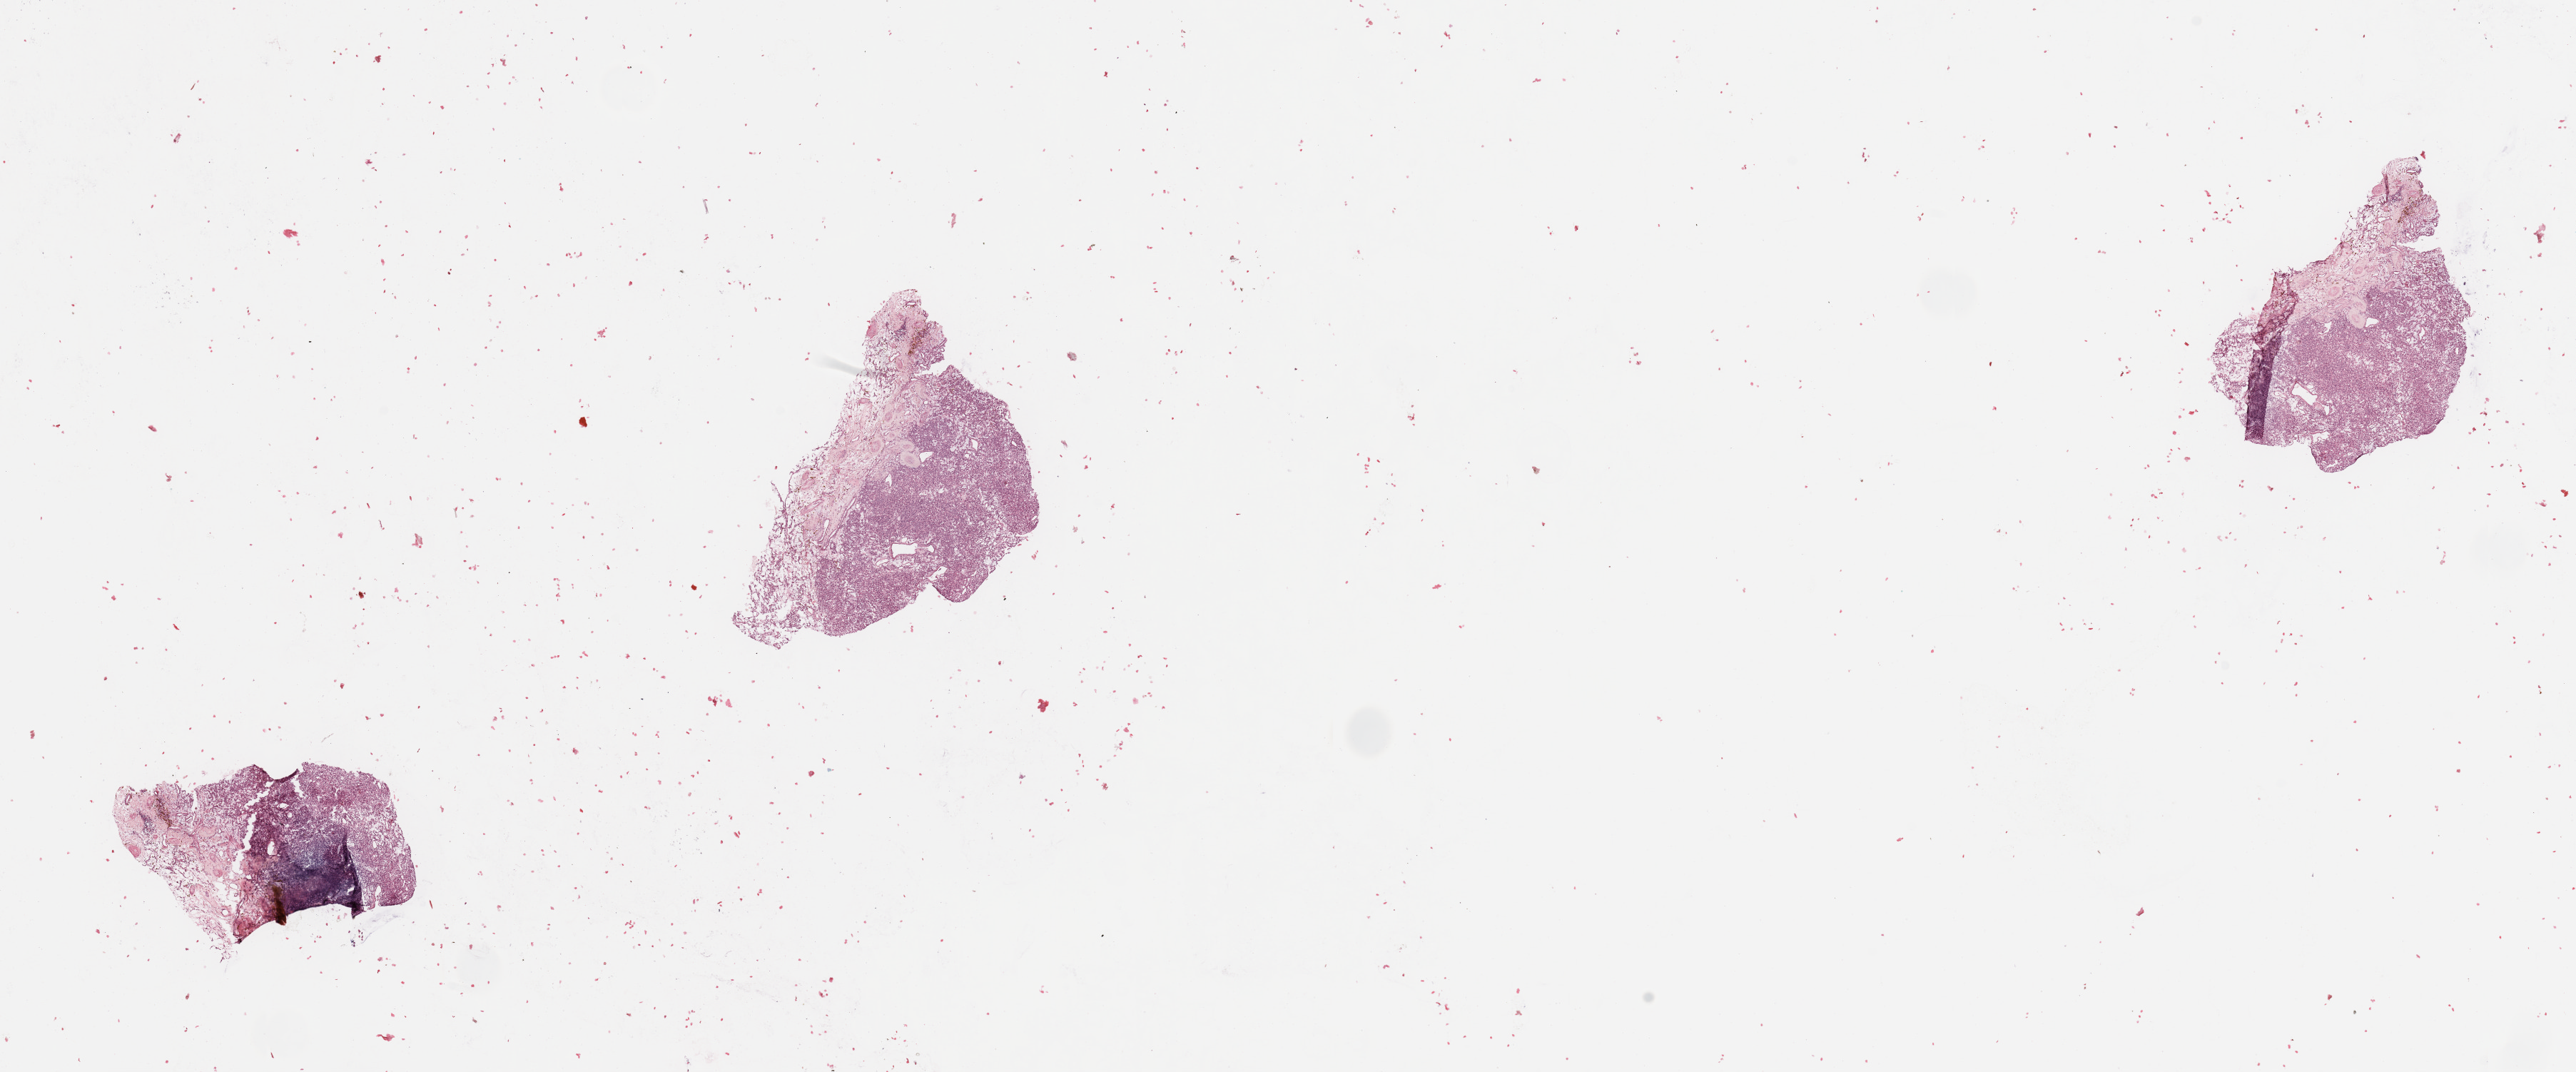
Whole-slide histology image, H&E — a low-resolution overview of the entire scanned area, about 28.5 x 11.9 mm, tumour tissue sample, sampled site: kidney. 56-year-old male patient. Histologic grade: G1 (well differentiated). Slide review estimates, as recorded: tumour nuclei 85%, necrosis 0%.
Primary tumour site (as recorded): middle. AJCC pathologic stage: I. Histologic diagnosis: Renal cell carcinoma, NOS.